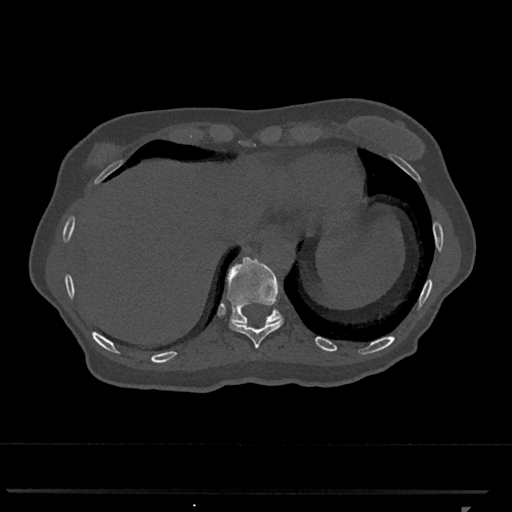
CT including the spine, one axial slice. Slice 550 of 793 in the series (ordered by position). Reconstruction kernel Br40s/3. Bone window (W 1800 / L 400 HU). 512 × 512 image matrix, field of view 380 × 380 mm. Female patient, age 62 years. Case-level facts recorded for this patient, not image findings: primary cancer: renal.
Structures marked on this image (semi-automatic segmentation, software-assisted and operator-edited):
- T10 vertebra: bounding box [x1, y1, x2, y2] px = [229, 318, 284, 349]
- T11 vertebra: [227, 257, 283, 325]